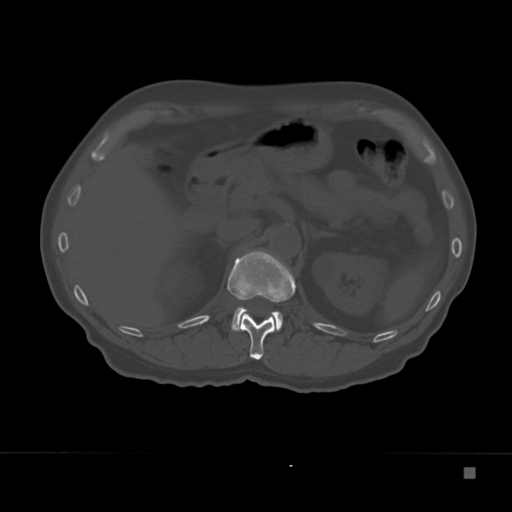
CT including the spine, one axial slice; position 124 of 332 along the scan axis; 120 kVp; bone window (W 1800 / L 400 HU); 1.5 mm slice thickness; 512 × 512 image matrix, field of view 389 × 389 mm. Male patient, age 72 years. From the clinical record (not read from this slice): primary cancer: skeletal.
Outlined on this slice (semi-automatically segmented with operator editing):
- L1 vertebra: bounding box <231,307,283,331> (left, top, right, bottom; pixels)
- T12 vertebra: <227,250,296,360>